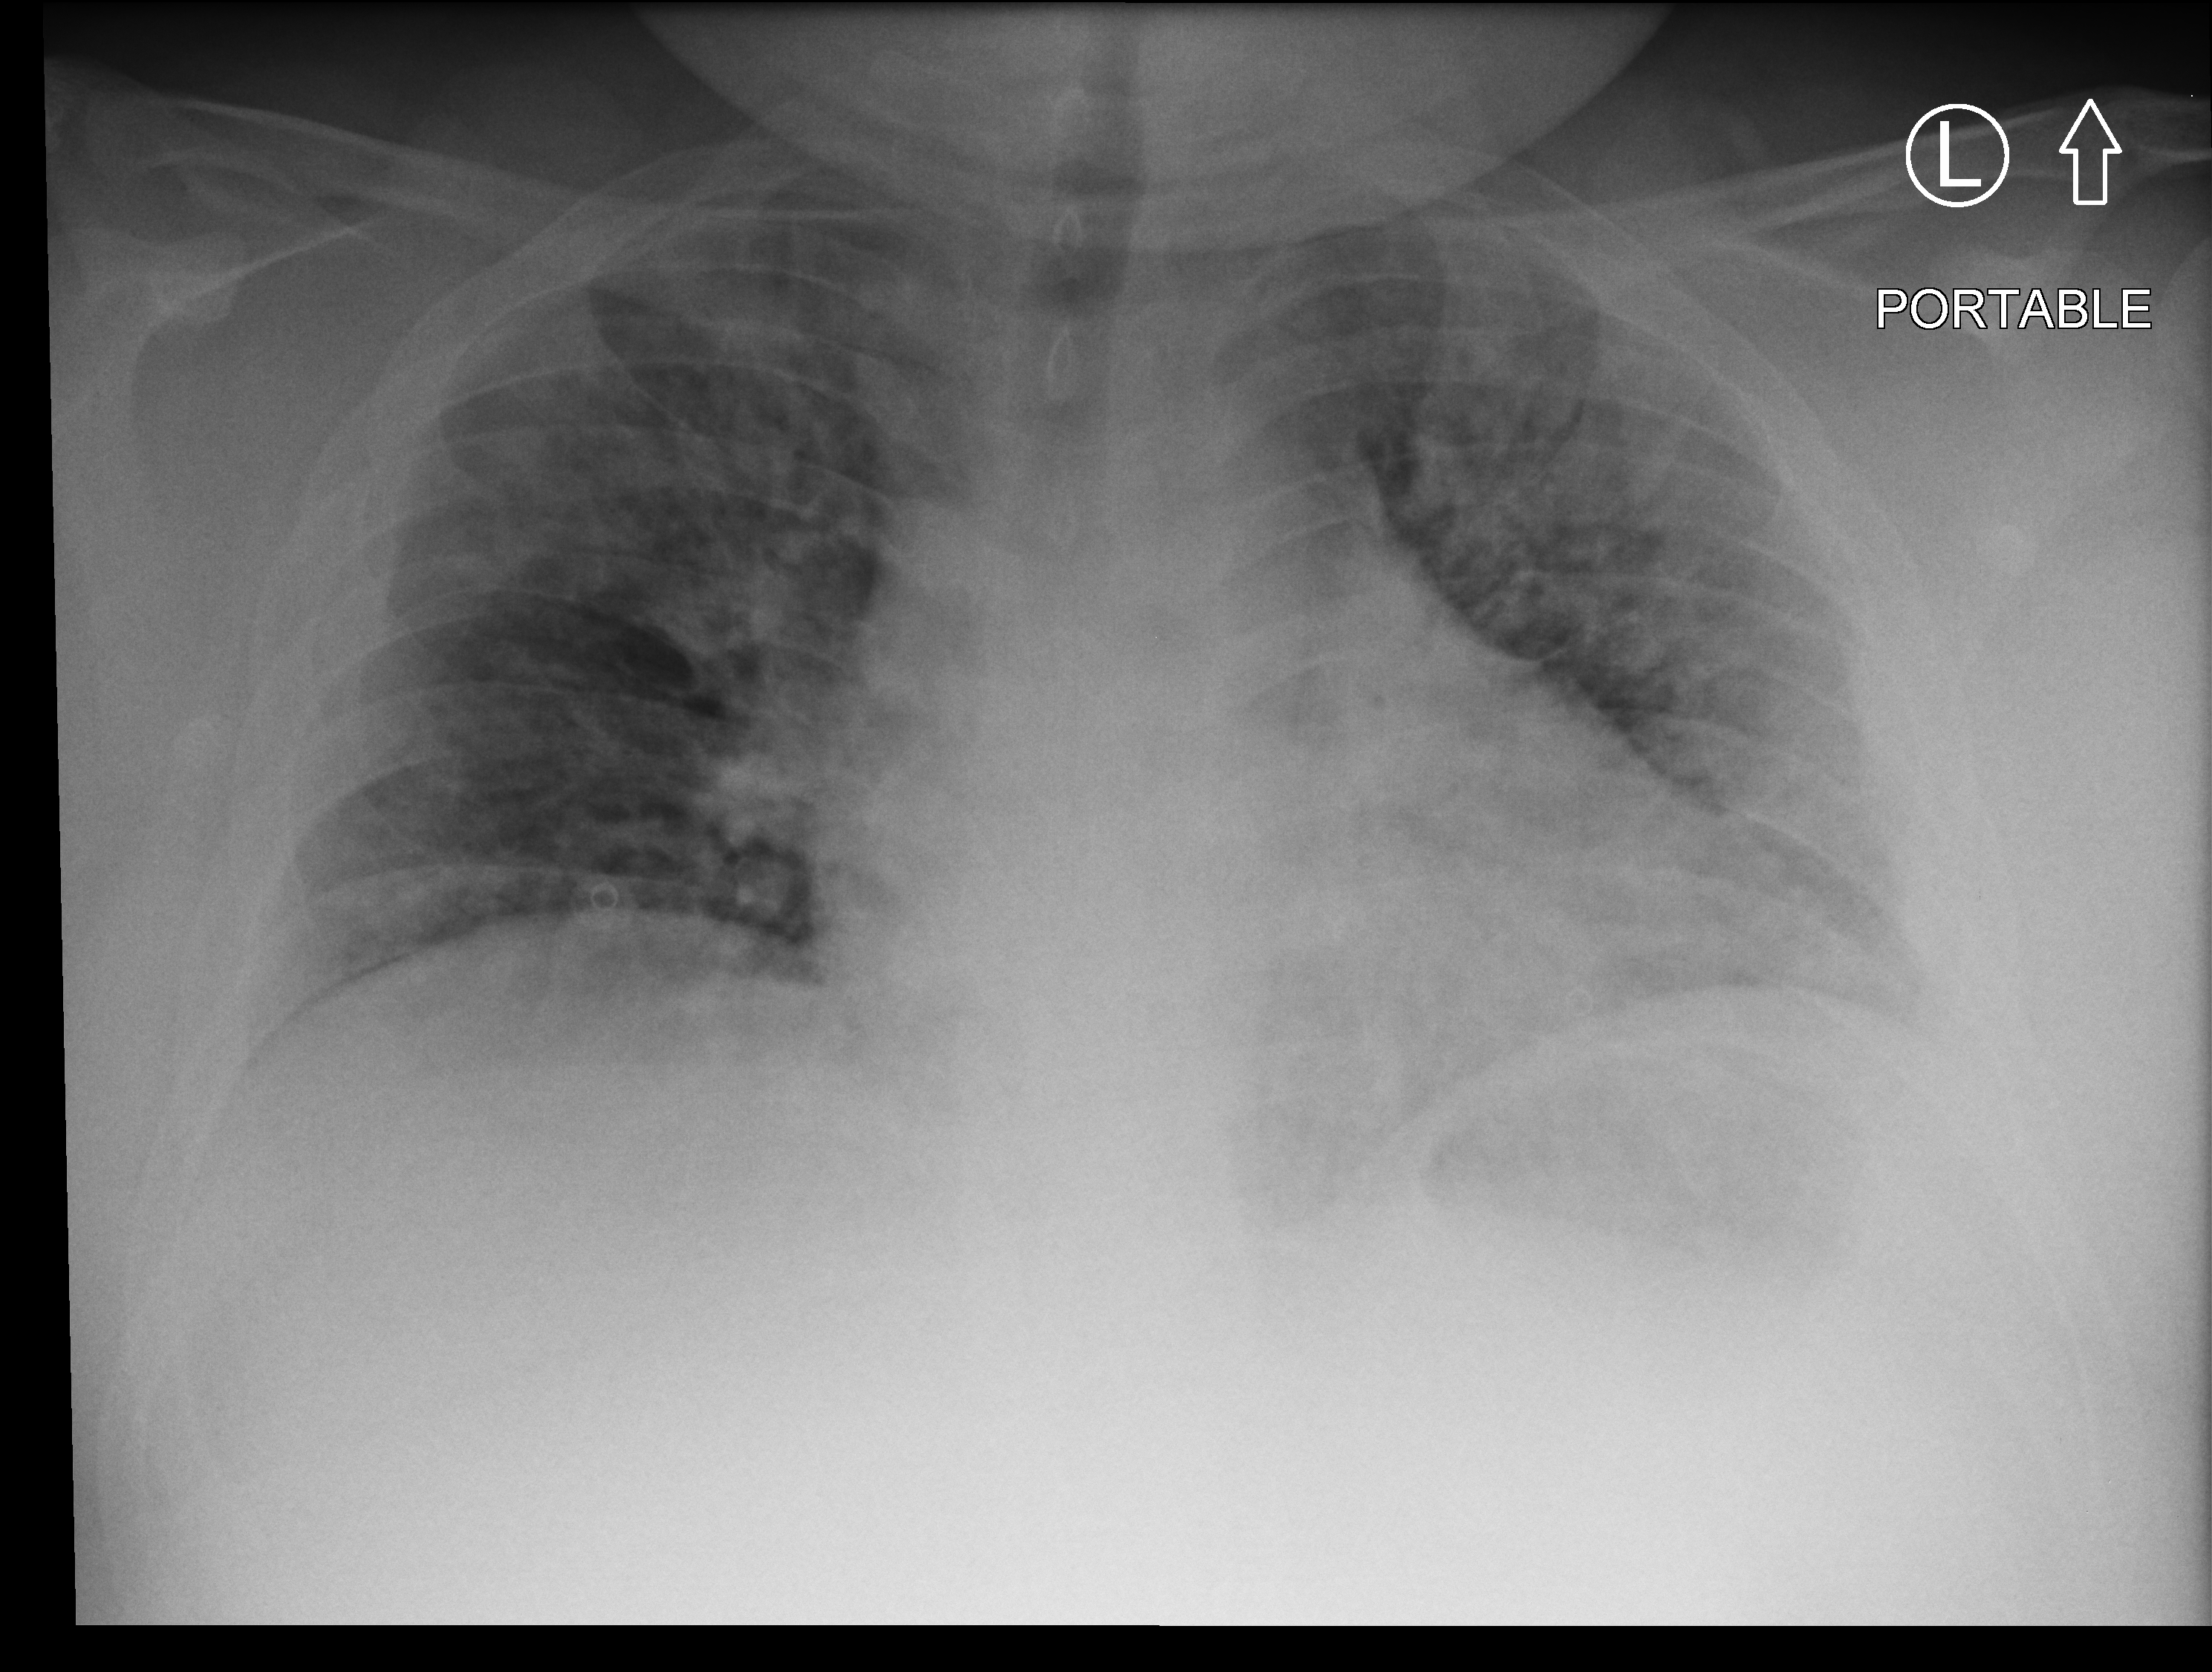
Portable chest radiograph. Patient hospitalised with COVID-19; male, aged 18–59 years.
Admission-level facts for this patient (not findings on this image; timing relative to this image not recorded):
- admitted to intensive care during this hospital stay: no
- length of hospital stay: 12 days
- mechanically ventilated during this hospital stay: no